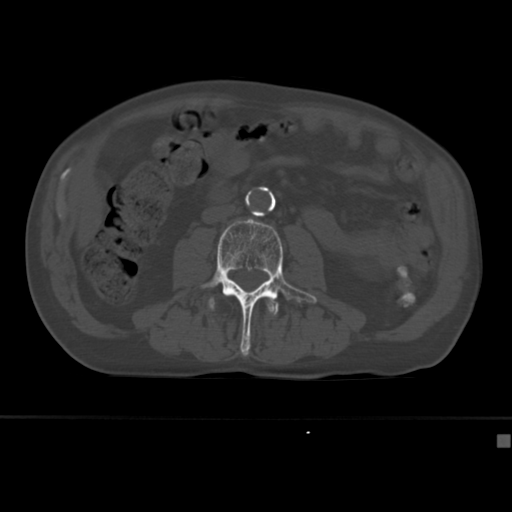
CT including the spine, one axial slice. Slice 128 of 430 in the series (ordered by position). Bone window (W 1800 / L 400 HU). 512 × 512 image matrix, field of view 337 × 337 mm. Male patient, age 64 years. Case-level facts recorded for this patient, not image findings: primary cancer: uterus.
Structures marked on this image (semi-automatic segmentation, software-assisted and operator-edited):
- L2 vertebra: bounding box [x1, y1, x2, y2] px = [266, 299, 277, 311]
- L3 vertebra: [200, 219, 317, 356]